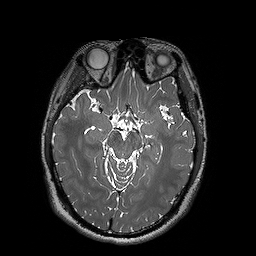
Brain MRI from a brain-tumour surgery series, one axial slice. Slice 102 of 192 in the series (ordered by position). 1 mm slice thickness. 256 × 256 image matrix, field of view 250 × 250 mm. Case-level facts recorded for this patient, not image findings: histopathology: Oligodendroglioma; WHO grade: 2; IDH mutation: yes.
Structures marked on this image (outlined manually by an expert reader):
- tumour: bounding box <159,159,193,161> (left, top, right, bottom; pixels)